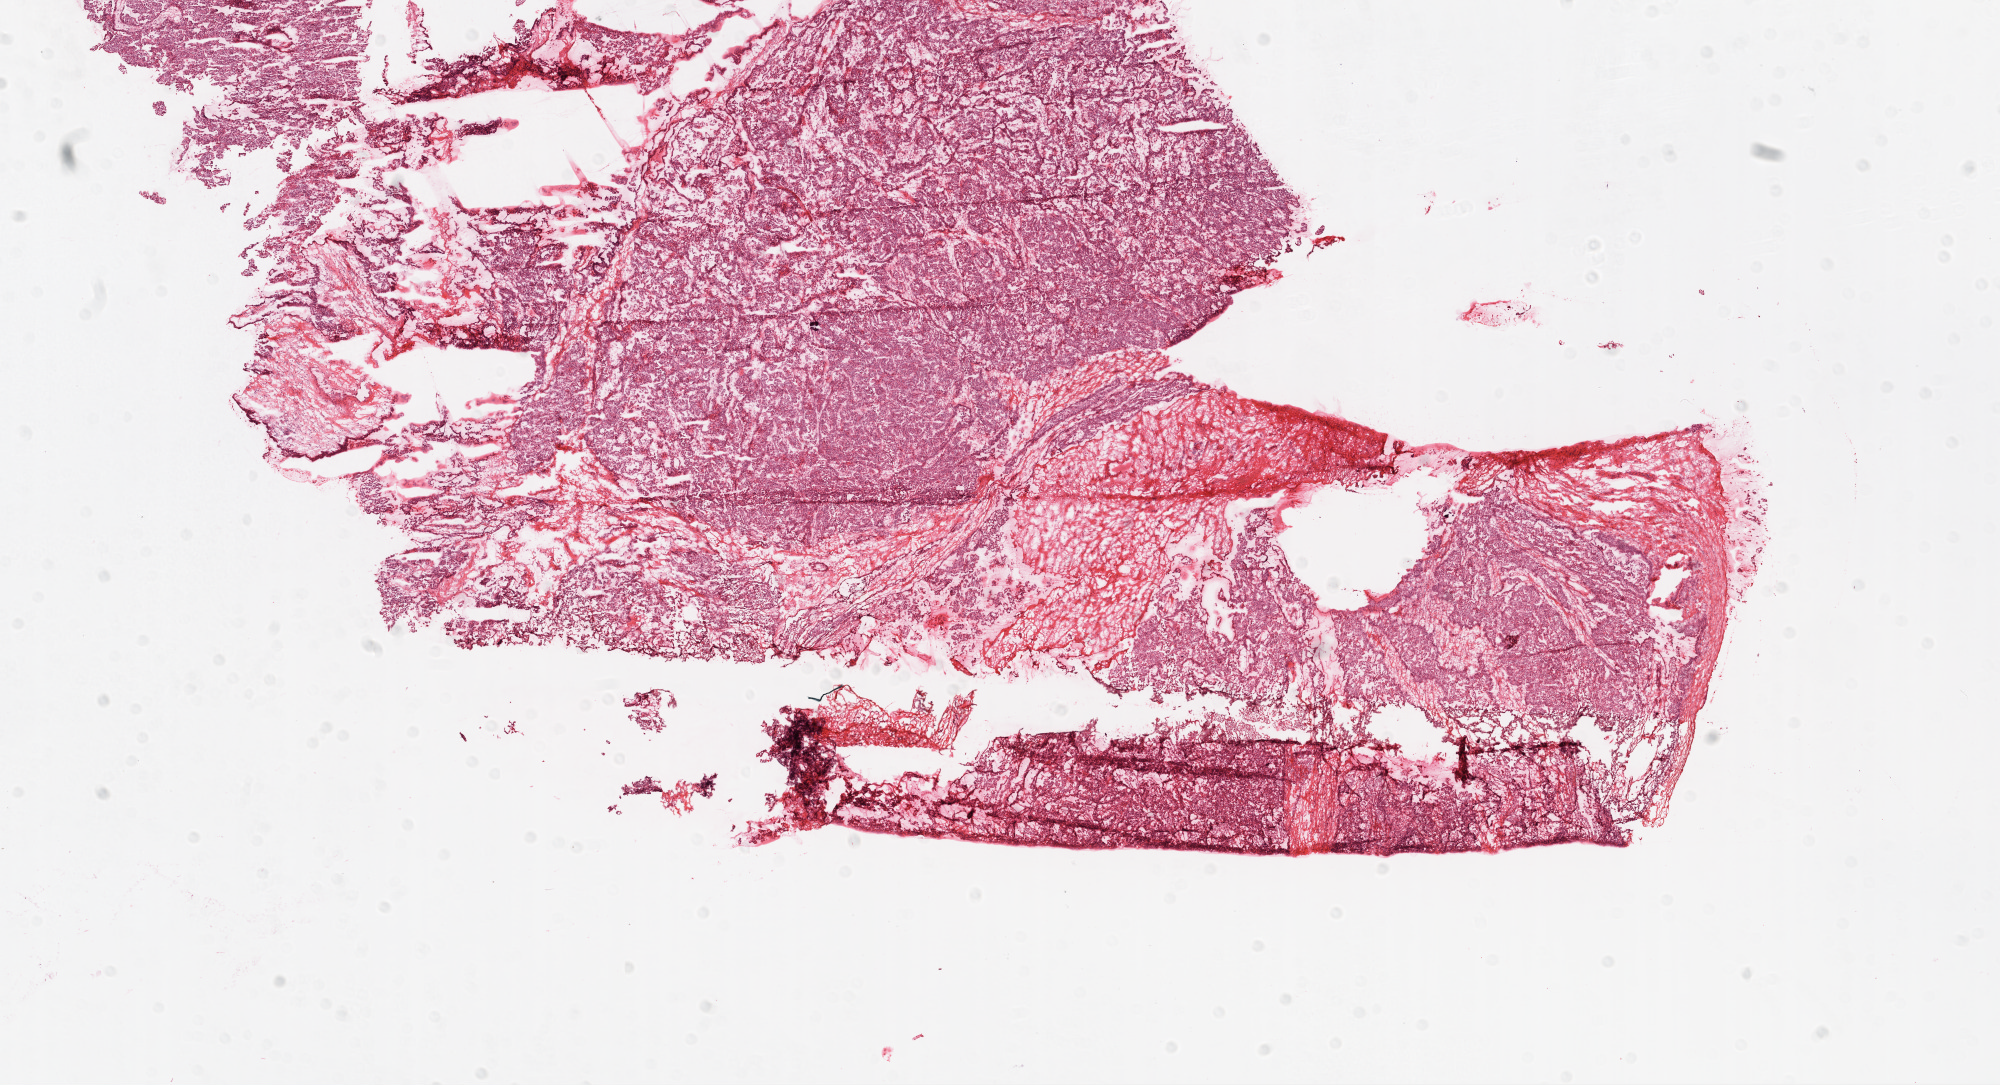
Whole-slide histology image, Hematoxylin and eosin (H&E) stained, low-resolution overview of the scanned area, about 16.0 x 8.7 mm (acquisition: 20x scan). Frozen section from the top of the tissue portion. Sample: primary tumour, ovary. Female, age 53 years at initial diagnosis. Histologic grade: G2 (moderately differentiated). Composition of this section per pathologist review: tumour cells 70%, tumour nuclei 85%, normal cells 12%, stromal cells 10%, necrosis 8%.
• diagnosis: Serous cystadenocarcinoma, NOS
• FIGO stage: IIC
• laterality: bilateral